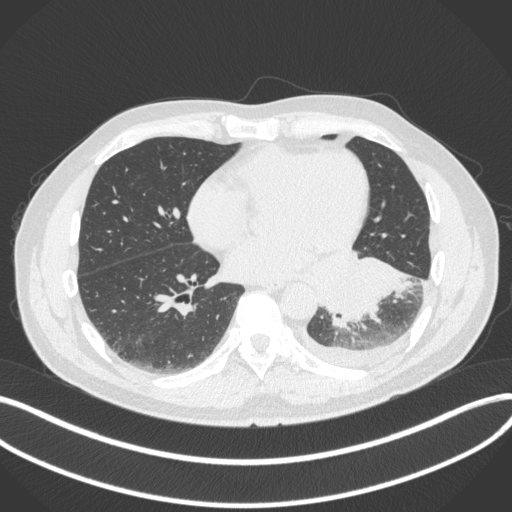
Chest CT, one axial slice; position 144 of 350 along the scan axis; lung window (W 1500 / L -600 HU); 512 × 512 image matrix, field of view 400 × 400 mm. Patient: male, 58 years. From the clinical record (not read from this slice): clinical TNM (as recorded): T3 N1 M1b.
Annotated regions visible in this slice (rectangle marked by the reading radiologist):
- lung tumour (recorded histology: small cell carcinoma): bounding box <327,257,415,334> (left, top, right, bottom; pixels)